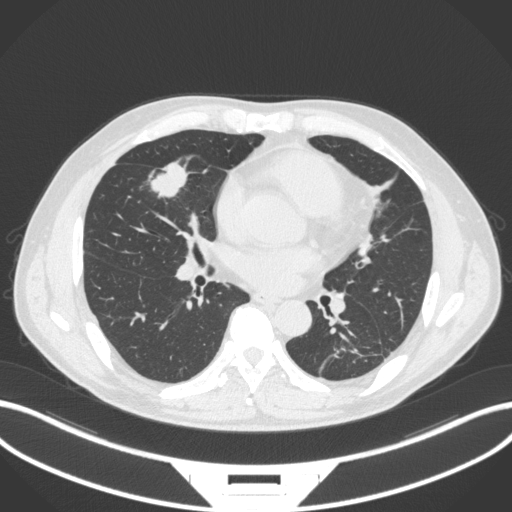
Chest CT, one axial slice. Slice 143 of 399 in the series (ordered by position). 120 kVp. Lung window (W 1500 / L -600 HU). 1 mm slice thickness. 512 × 512 image matrix, field of view 400 × 400 mm. Male patient, age 59 years. From the clinical record (not read from this slice): clinical TNM (as recorded): T2a N1 M0.
Annotated regions visible in this slice (rectangle marked by the reading radiologist):
- lung tumour (recorded histology: adenocarcinoma): bounding box <144,158,191,201> (left, top, right, bottom; pixels)